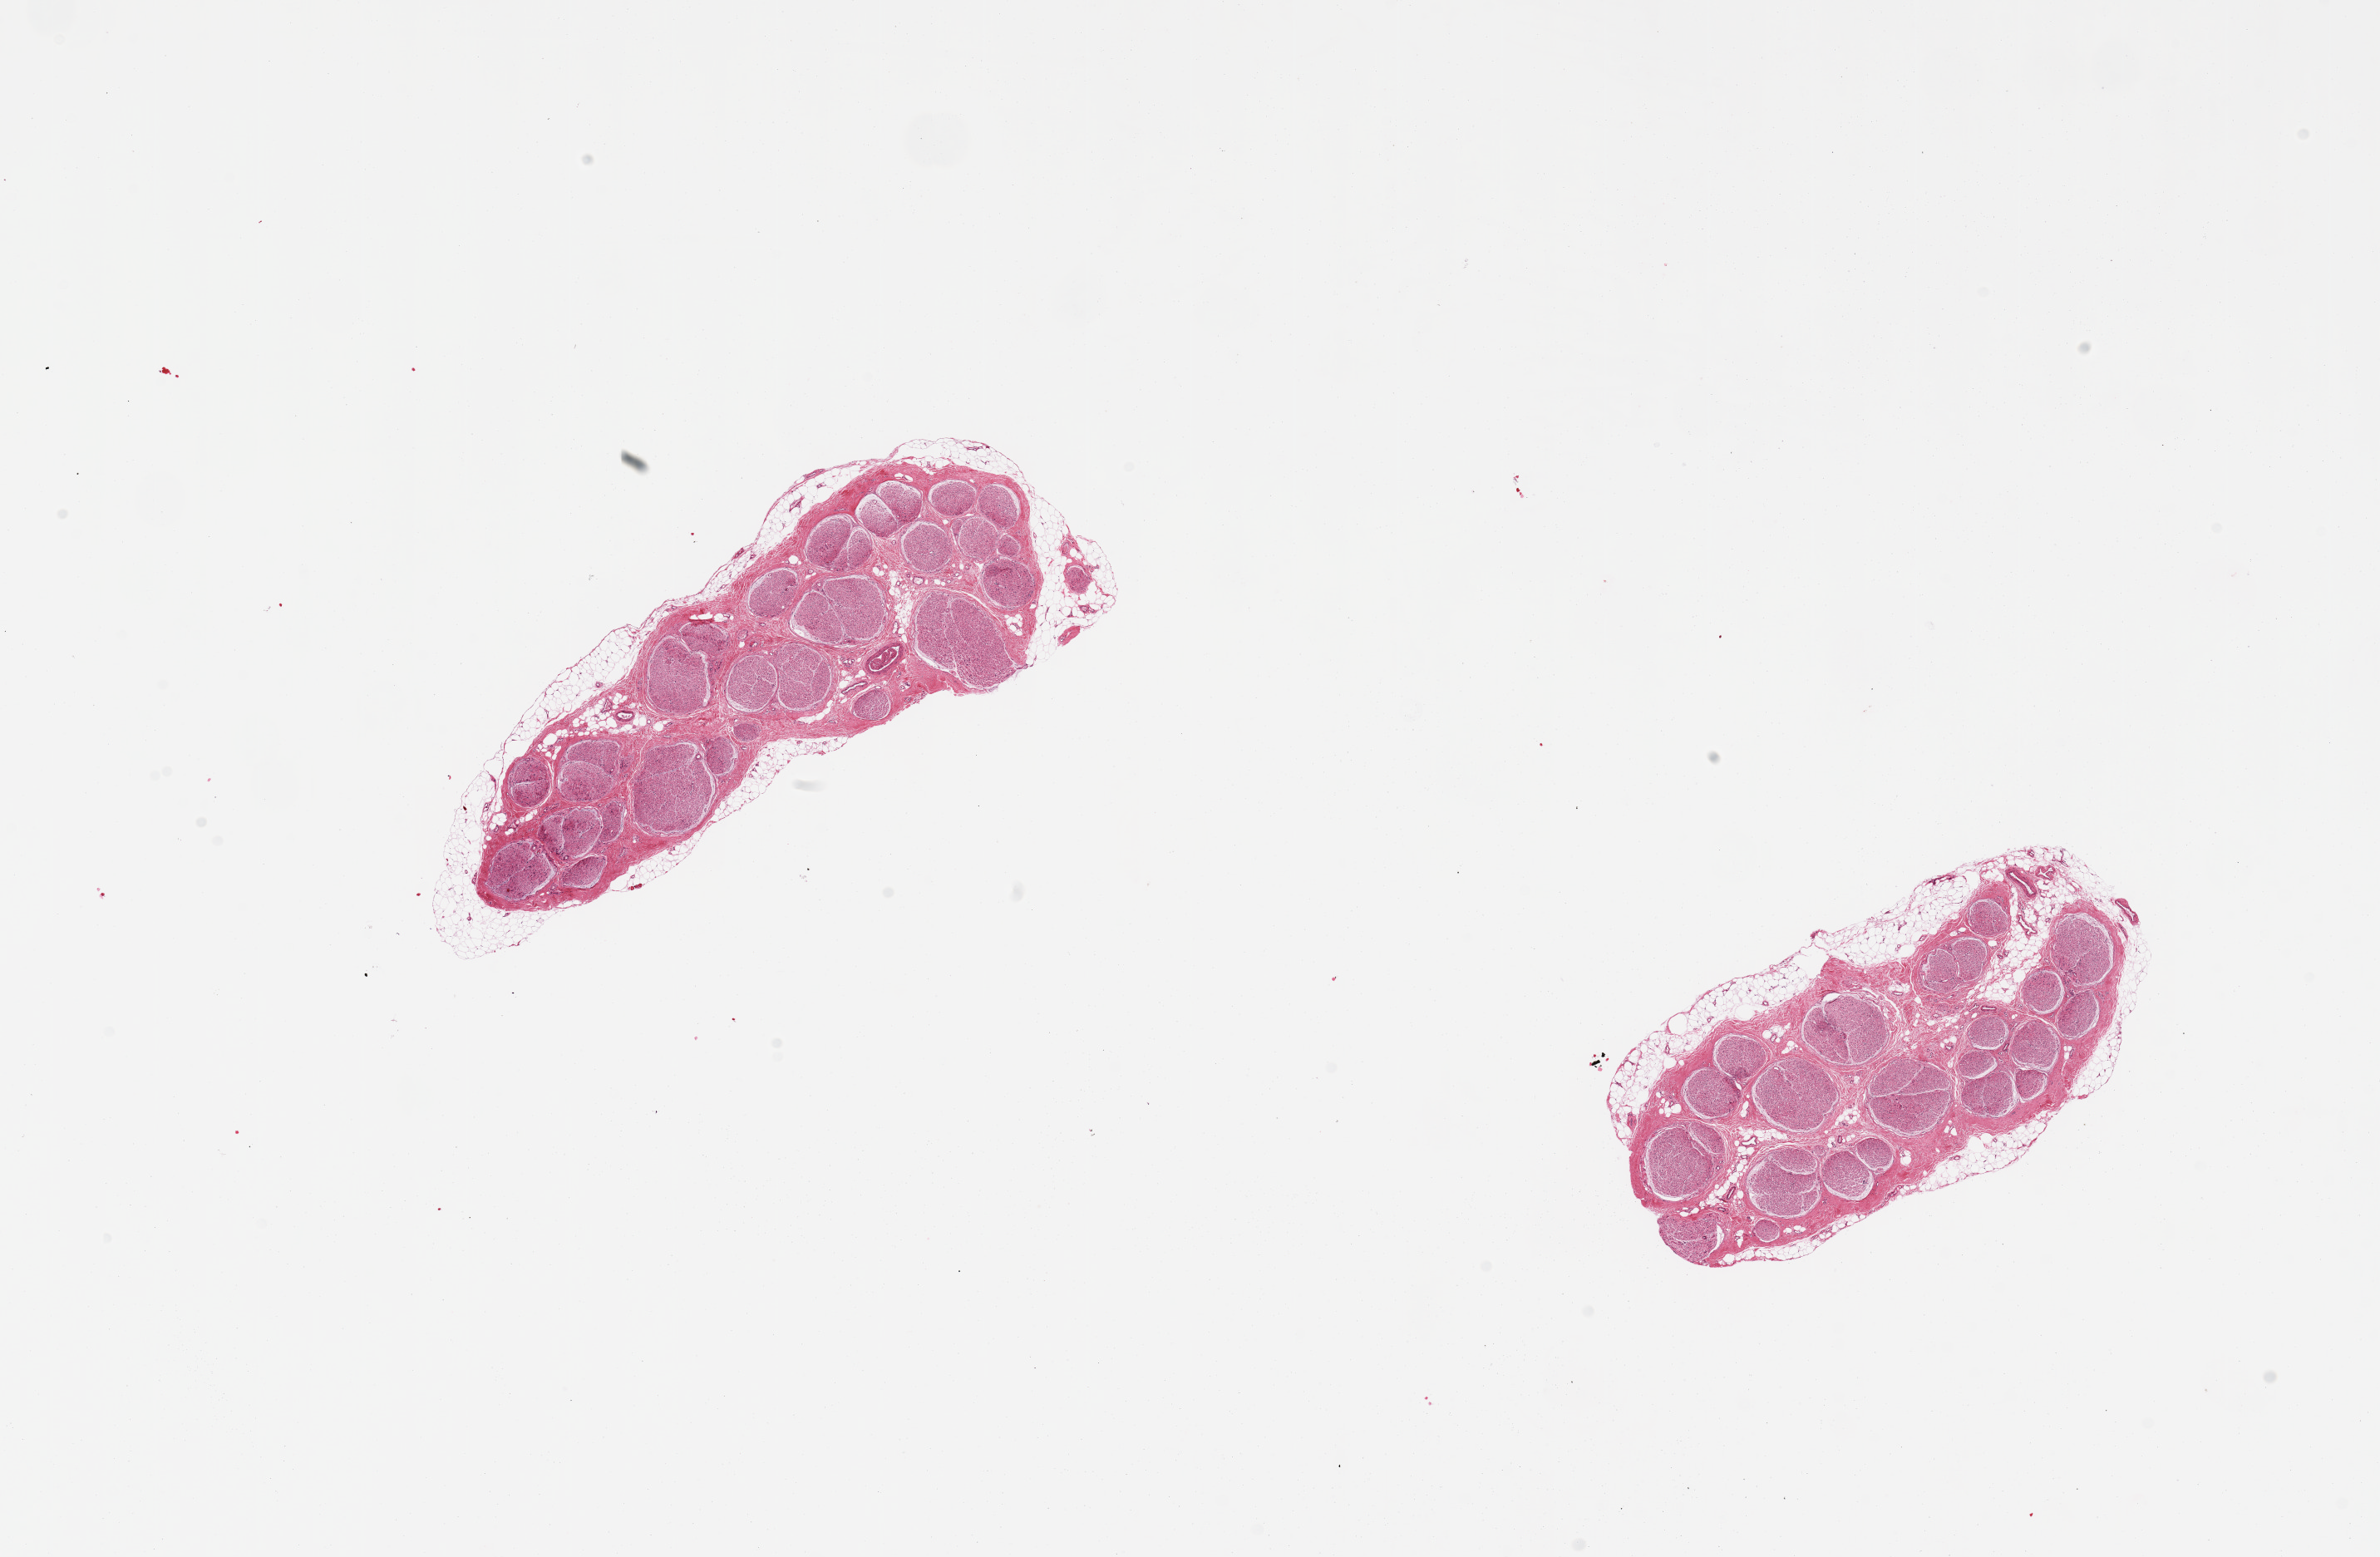
Whole-slide image, haematoxylin and eosin stain — low-resolution overview of the scanned area, about 22.6 x 14.8 mm. PAXgene-fixed, paraffin-embedded tissue. Section of tibial nerve (target tissue). Tissue donor sample. Female donor.
Reviewer comment on this tissue sample: 2 pieces; 0.4 mm fat surrounding each piece.